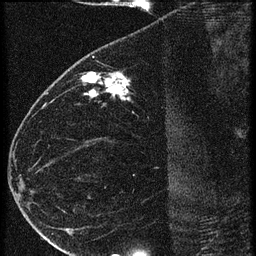
Breast MRI (dynamic contrast-enhanced), one sagittal slice; position 25 of 60 along the scan axis; 3 images stored at this slice position (order not interpretable as contrast timing); 1.5 T; TE 4.2 ms, TR 20.4 ms; 1.5 mm slice thickness; 256 × 256 image matrix. Patient: female, 35 years. Case-level facts recorded for this patient, not image findings: setting: breast cancer imaged before/during neoadjuvant chemotherapy; receptor status: HR-positive, HER2-negative.
Annotated regions visible in this slice (semi-automatic segmentation, software-assisted and operator-edited):
- analysis volume of interest (the breast-tissue region the enhancement analysis was run in; not a lesion): box from (x=65, y=60) to (x=169, y=119) px
- tumour enhancement mask (voxels above the 90 % enhancement threshold inside the analysis volume of interest): (x=80, y=72)–(x=129, y=97)